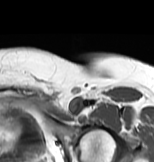
MRI of an extremity soft-tissue mass, one axial slice; MR volume resampled by the dataset authors to the PET/CT grid (not the native acquisition matrix); 154 × 162 image matrix, field of view 150 × 158 mm. Female patient. Case-level facts recorded for this patient, not image findings: histological type: myxofibrosarcoma; grade: intermediate; site of the primary tumour: left thigh.
Outlined on this slice (expert contour drawn on MRI and transferred to this co-registered scan by the dataset authors):
- gross tumour volume including surrounding oedema: bounding box (x1, y1, x2, y2) in pixels: (72, 103, 82, 113)